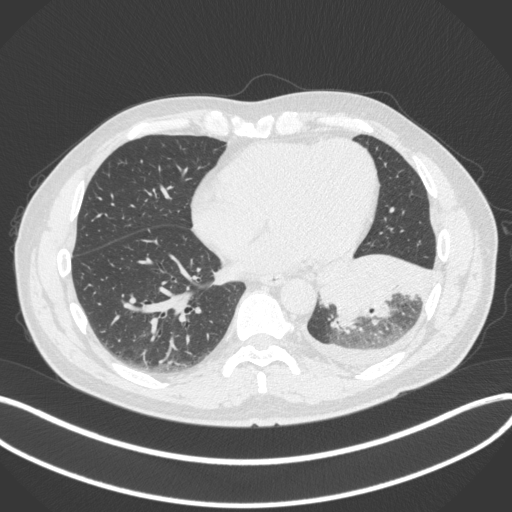
Chest CT, one axial slice; position 126 of 350 along the scan axis; lung window (W 1500 / L -600 HU); 1 mm slice thickness; 512 × 512 image matrix, field of view 400 × 400 mm. Patient: male, 58 years. From the clinical record (not read from this slice): clinical TNM (as recorded): T3 N1 M1b.
Structures marked on this image (rectangle marked by the reading radiologist):
- lung tumour (recorded histology: small cell carcinoma): bounding box <316,242,437,335> (left, top, right, bottom; pixels)